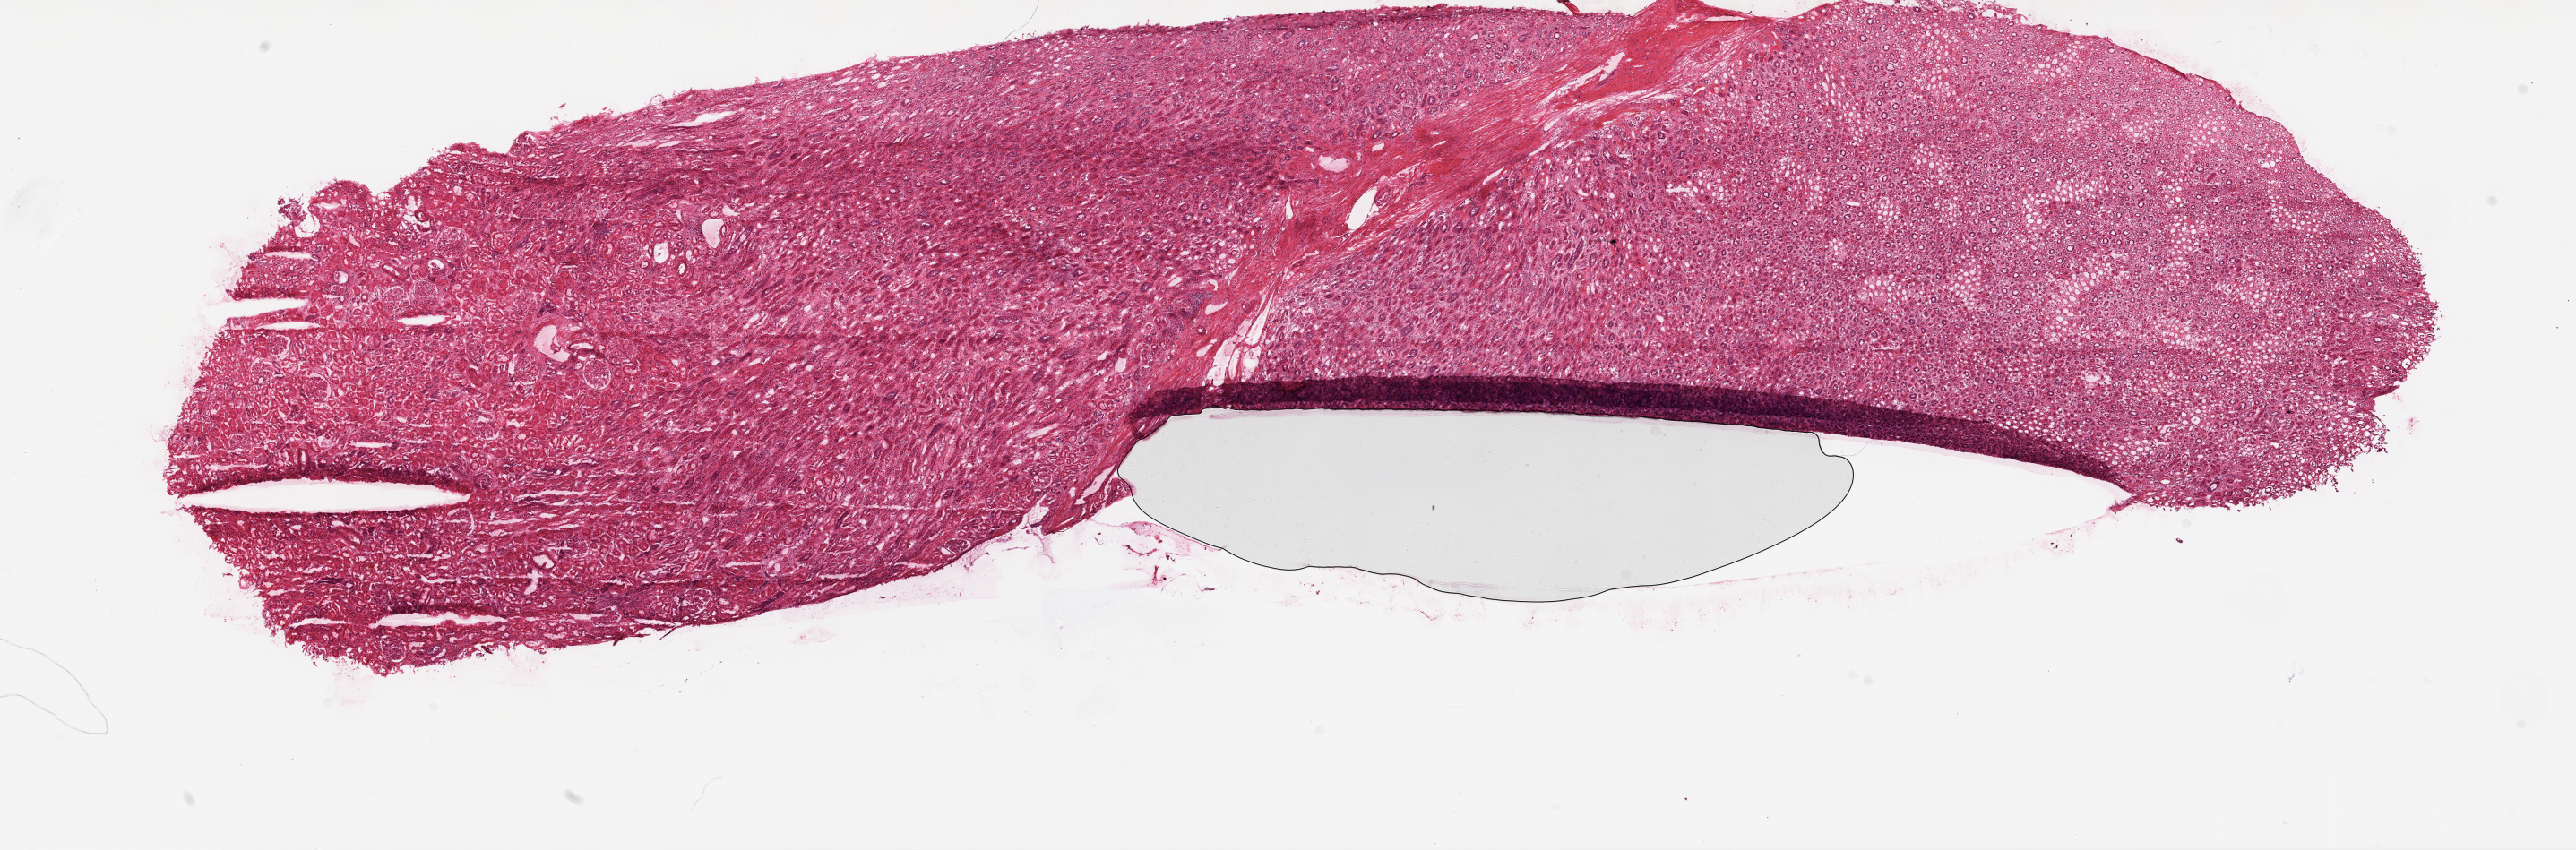
Whole-slide histology image, H&E-stained, low-resolution overview of the scanned area, about 23.1 x 7.6 mm (from a 20x scan). Frozen section. Kidney, solid tissue normal (non-tumour tissue) sample. Male patient; age at initial diagnosis 45 years.
This section: solid tissue normal sample (biorepository sample class). Patient diagnosis: Clear cell adenocarcinoma, NOS.